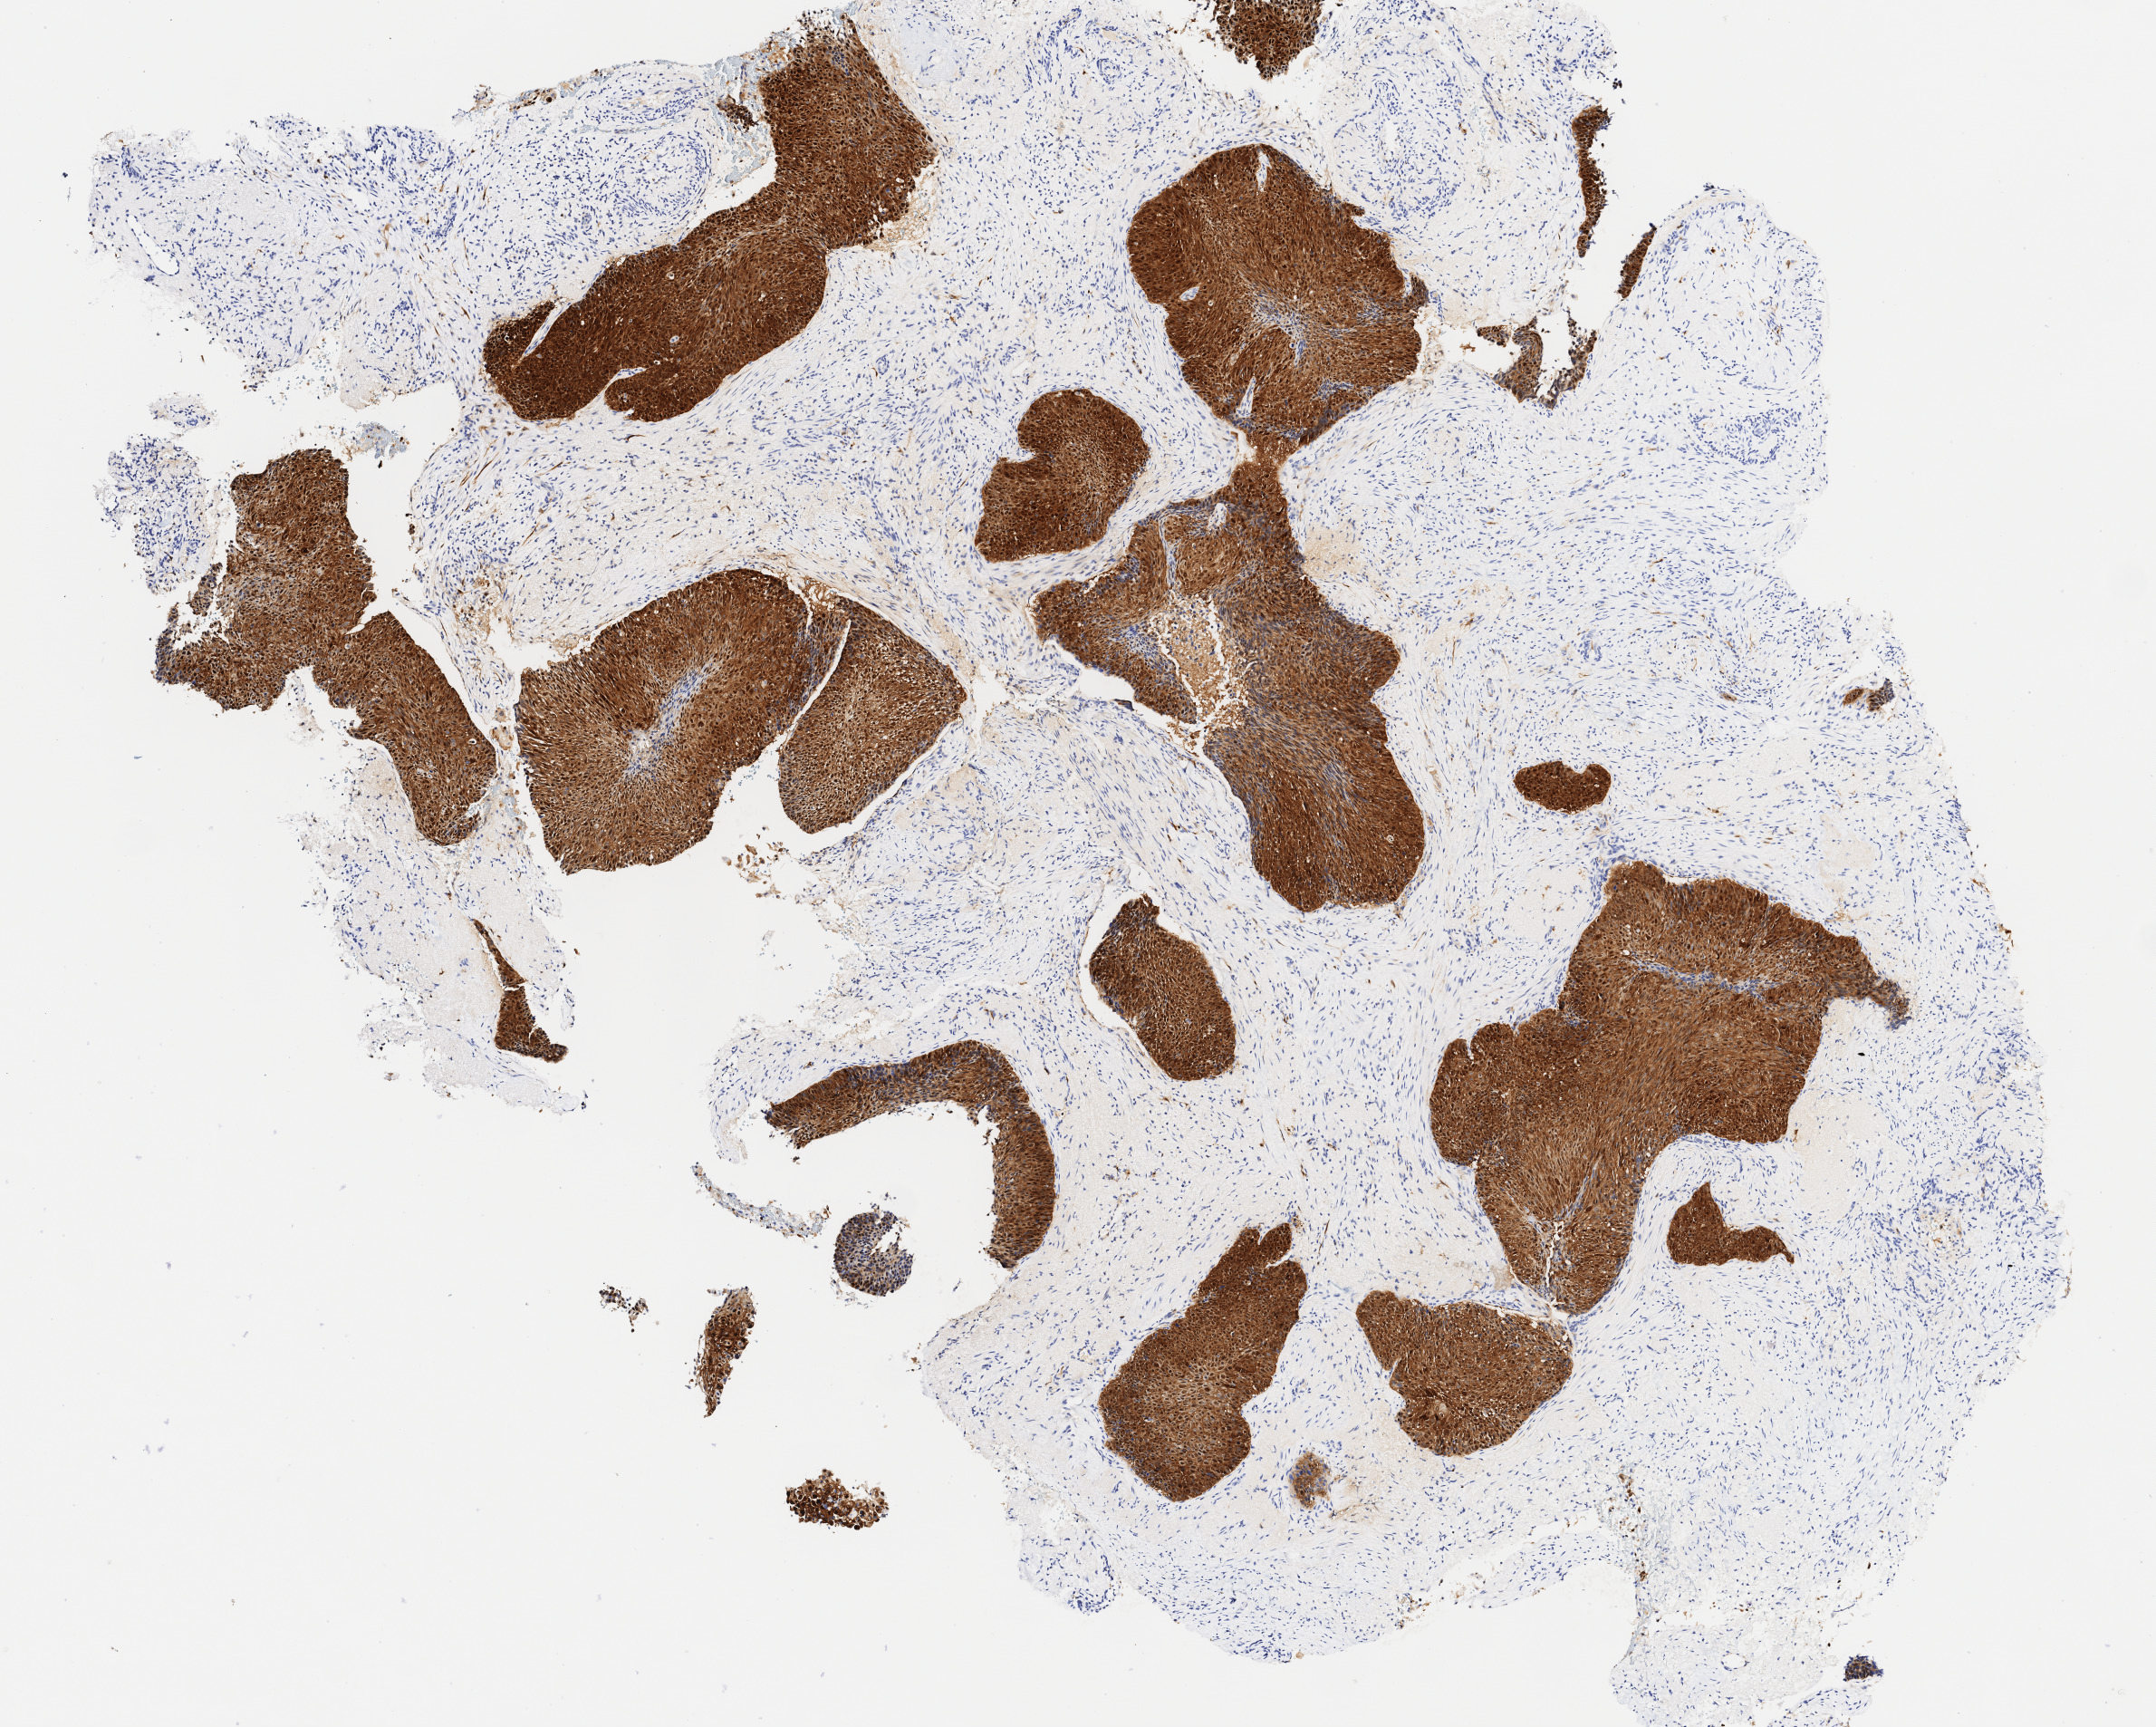
Whole-slide image, immunohistochemical stain for p16 (p16INK4a) — a low-resolution overview of the entire scanned area, about 4.7 x 3.8 mm. Tumor tissue. Anatomic site: cervix. Patient: female, aged 48.
* diagnosis: Squamous cell carcinoma, large cell, nonkeratinizing, NOS